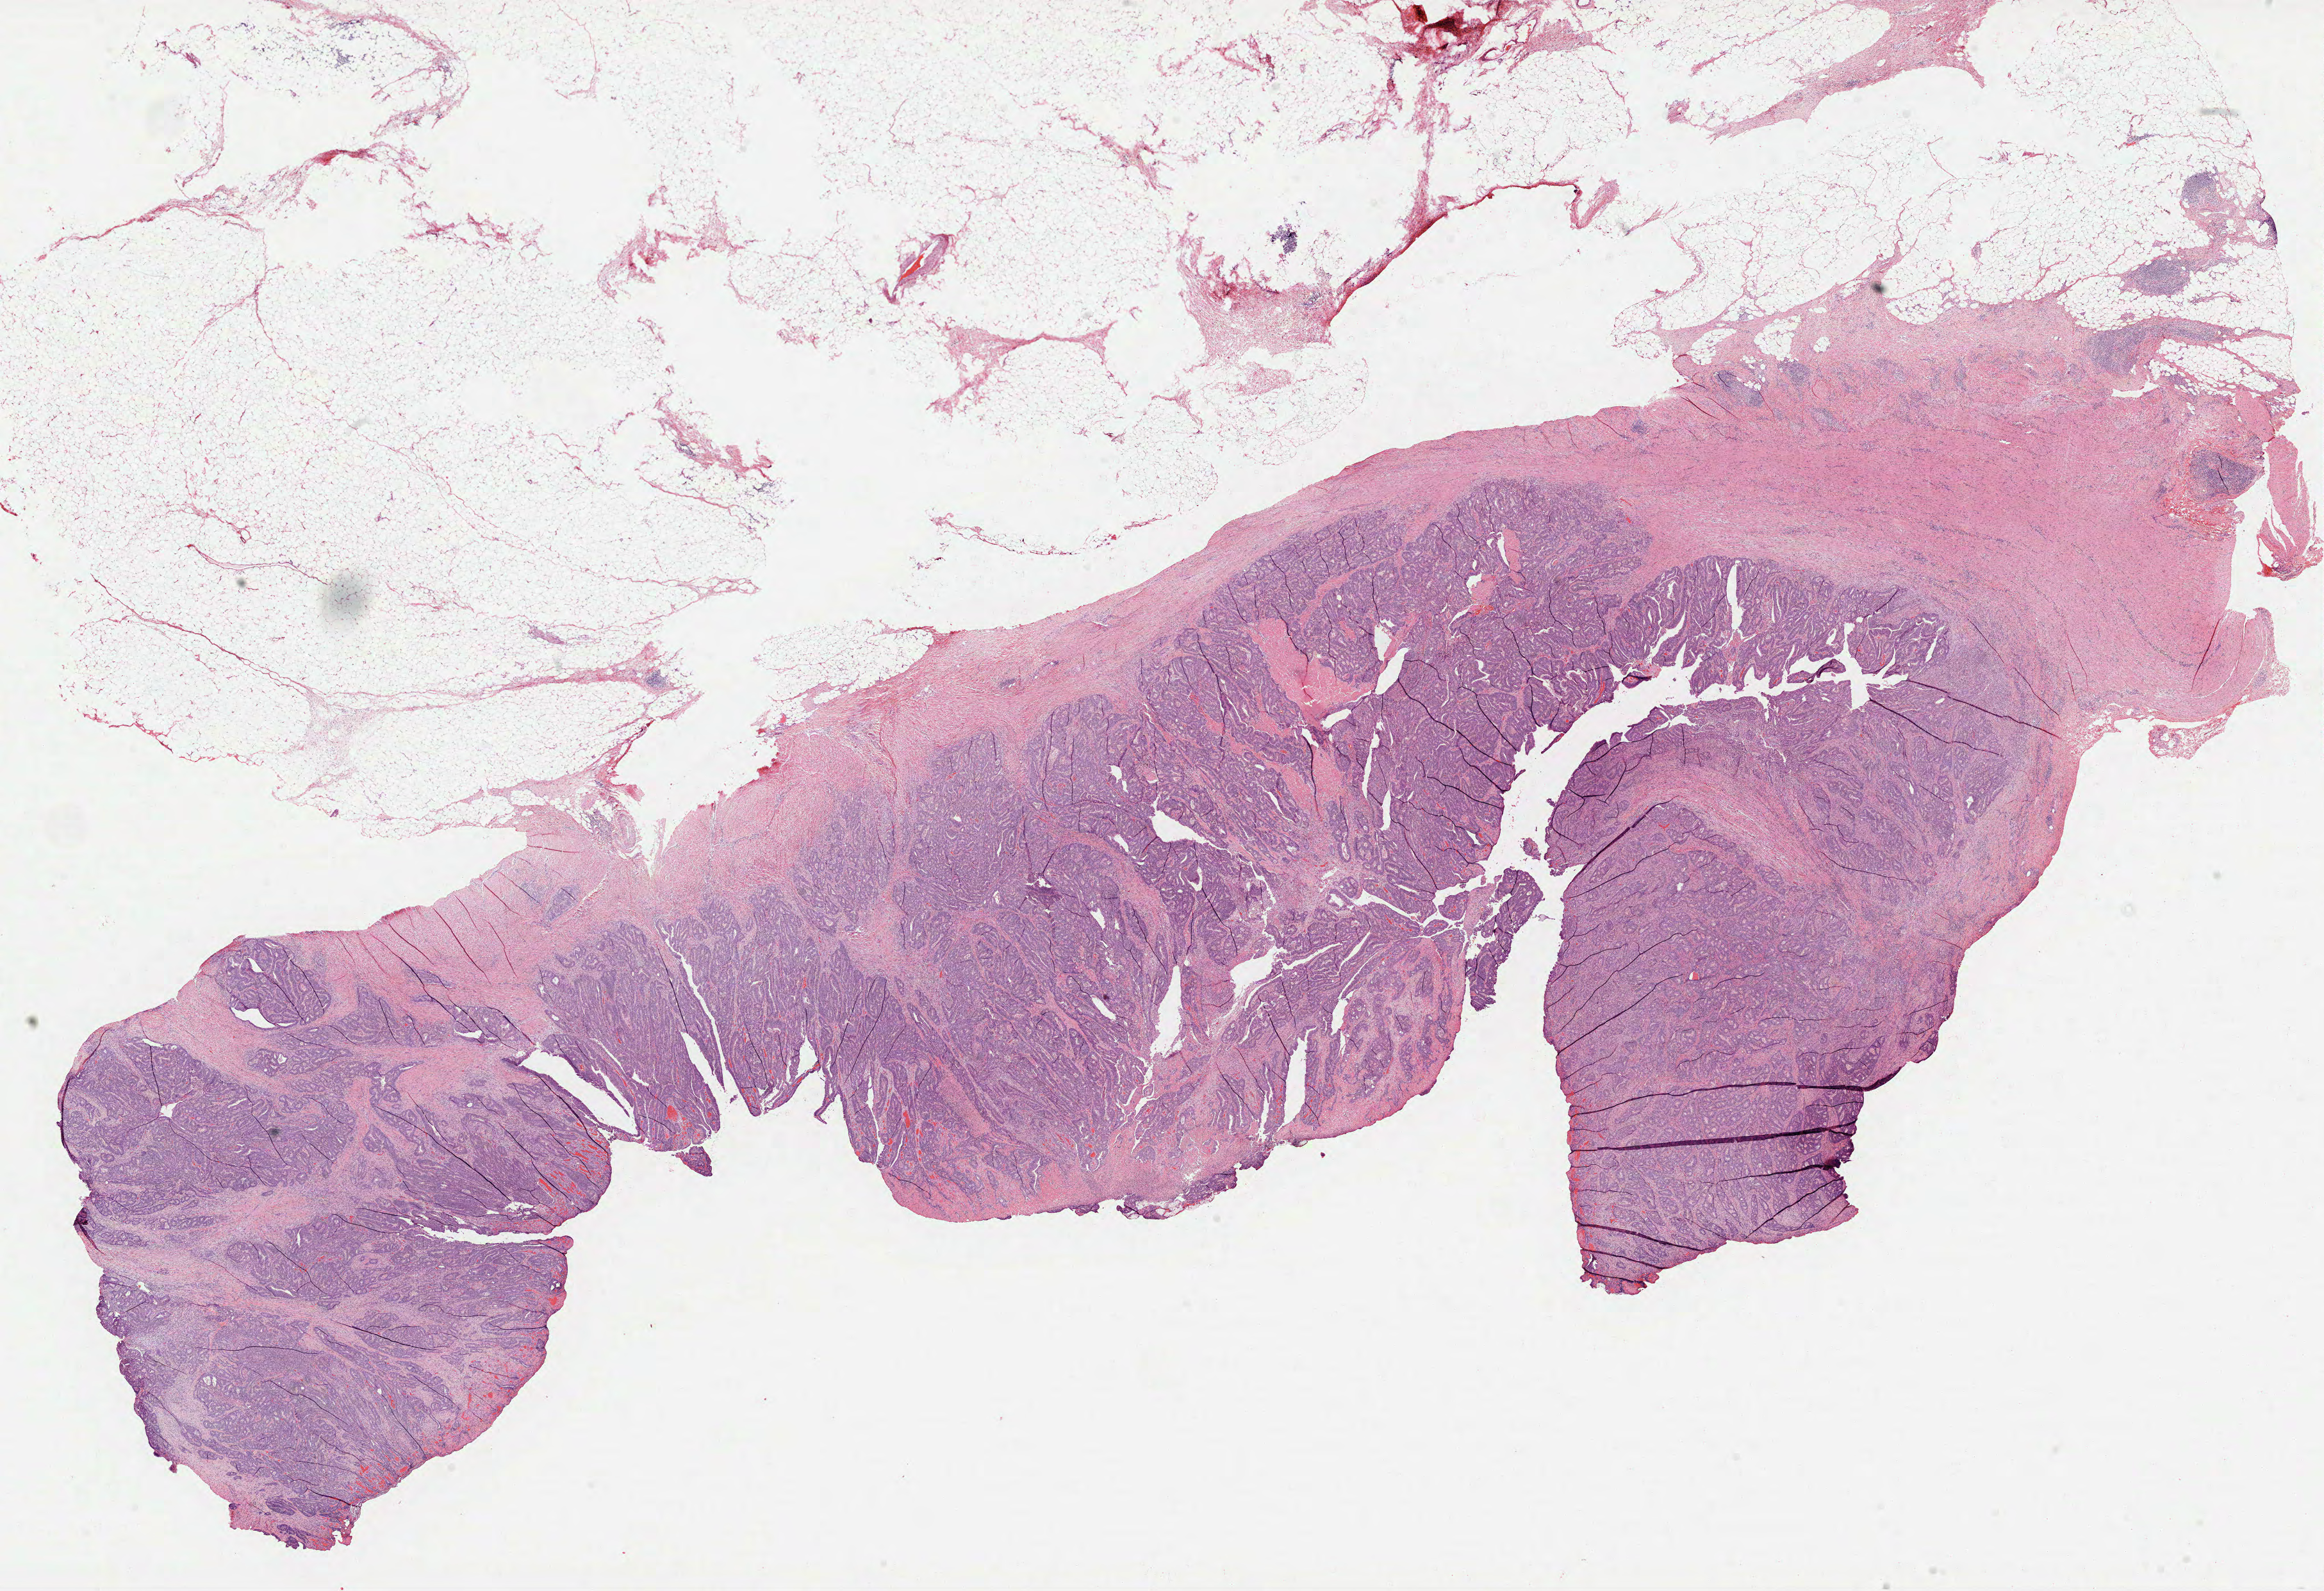
H&E-stained whole-slide image, low-resolution overview of the scanned area, about 29.2 x 20.0 mm (slide scanned at 40x); formalin-fixed paraffin-embedded (FFPE) diagnostic section; sample: primary tumour, colon. Female patient; age at initial diagnosis 51 years.
- lymph nodes positive (case pathology): 6 of 109 examined
- pathologic diagnosis: Adenocarcinoma, NOS
- AJCC pathologic stage: IIIC (6th edition)